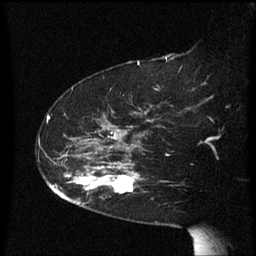
Breast MRI (dynamic contrast-enhanced), one sagittal slice. Slice 43 of 60 in the series (ordered by position). Dynamic contrast-enhanced series, image 2 of 3 at this slice position (ordered by acquisition). 1.5 T. TE 4.2 ms, TR 8.4 ms. 2.3 mm slice thickness. 256 × 256 image matrix, field of view 200 × 200 mm. Patient: female, 63 years. From the clinical record (not read from this slice): setting: breast cancer imaged before/during neoadjuvant chemotherapy; receptor status: HER2-positive.
Outlined on this slice (semi-automatic segmentation, software-assisted and operator-edited):
- analysis volume of interest (the breast-tissue region the enhancement analysis was run in; not a lesion): bounding box (x1, y1, x2, y2) in pixels: (71, 144, 146, 207)
- tumour enhancement mask (voxels above the 70 % enhancement threshold inside the analysis volume of interest): (71, 168, 138, 195)